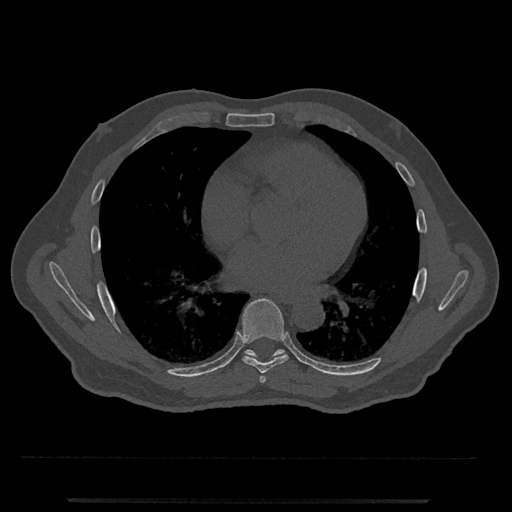
CT including the spine, one axial slice; position 669 of 797 along the scan axis; reconstruction kernel Br40s/3; bone window (W 1800 / L 400 HU); 0.5 mm slice thickness; 512 × 512 image matrix. Male patient, age 63 years. Case-level facts recorded for this patient, not image findings: primary cancer: prostate.
Outlined on this slice (semi-automatic segmentation, software-assisted and operator-edited):
- T6 vertebra: box from (x=259, y=376) to (x=266, y=383) px
- T7 vertebra: (x=240, y=298)–(x=289, y=374)
- T8 vertebra: (x=244, y=349)–(x=285, y=357)